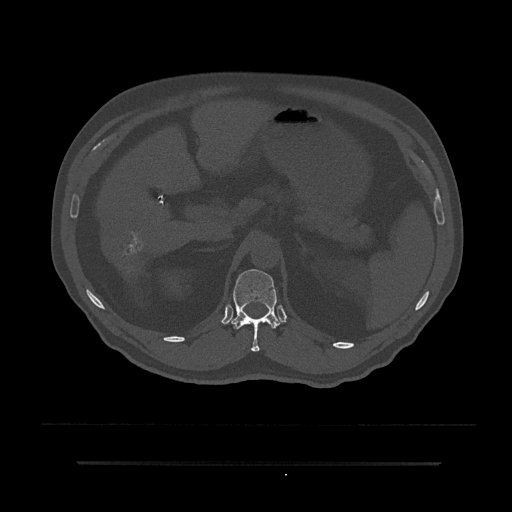
CT including the spine, one axial slice; slice 213 of 797 in the series (ordered by position); 120 kVp; bone window (W 1800 / L 400 HU); 0.5 mm slice thickness; 512 × 512 image matrix. Male patient, age 59 years. Case-level facts recorded for this patient, not image findings: primary cancer: bile ducts; vertebrae with lytic lesions (as recorded): T10.
Annotated regions visible in this slice (semi-automatic segmentation, software-assisted and operator-edited):
- T12 vertebra: box from (x=231, y=269) to (x=280, y=352) px